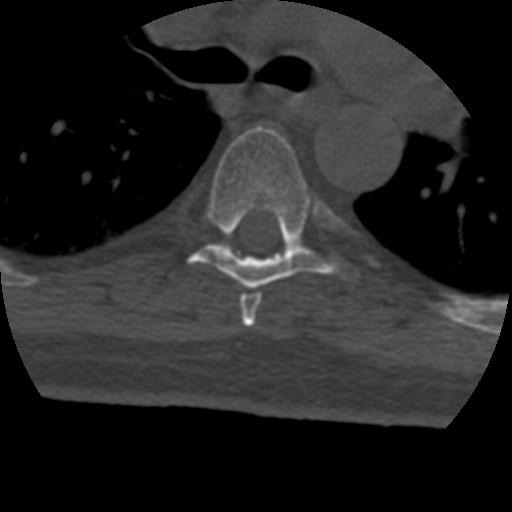
CT including the spine, one axial slice. Slice 301 of 399 in the series (ordered by position). 120 kVp. Bone window (W 1800 / L 400 HU). 1.25 mm slice thickness. 512 × 512 image matrix, field of view 160 × 160 mm. Patient age 69 years. From the clinical record (not read from this slice): primary cancer: prostate.
Outlined on this slice (semi-automatically segmented with operator editing):
- T5 vertebra: bounding box [x1, y1, x2, y2] px = [240, 289, 262, 327]
- T6 vertebra: [190, 127, 358, 289]
- T7 vertebra: [218, 246, 228, 250]